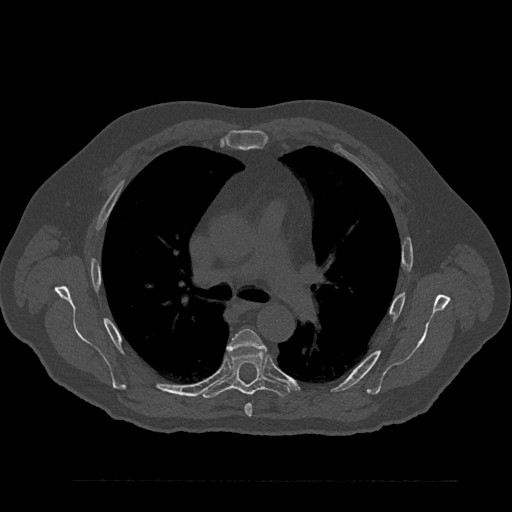
CT including the spine, one axial slice. Slice 571 of 797 in the series (ordered by position). Reconstruction kernel Br40s/3. 120 kVp. Bone window (W 1800 / L 400 HU). 512 × 512 image matrix. Male patient, age 61 years. Case-level facts recorded for this patient, not image findings: primary cancer: prostate.
Annotated regions visible in this slice (semi-automatic segmentation, software-assisted and operator-edited):
- T5 vertebra: bounding box [x1, y1, x2, y2] px = [228, 328, 265, 417]
- T6 vertebra: [201, 350, 290, 399]